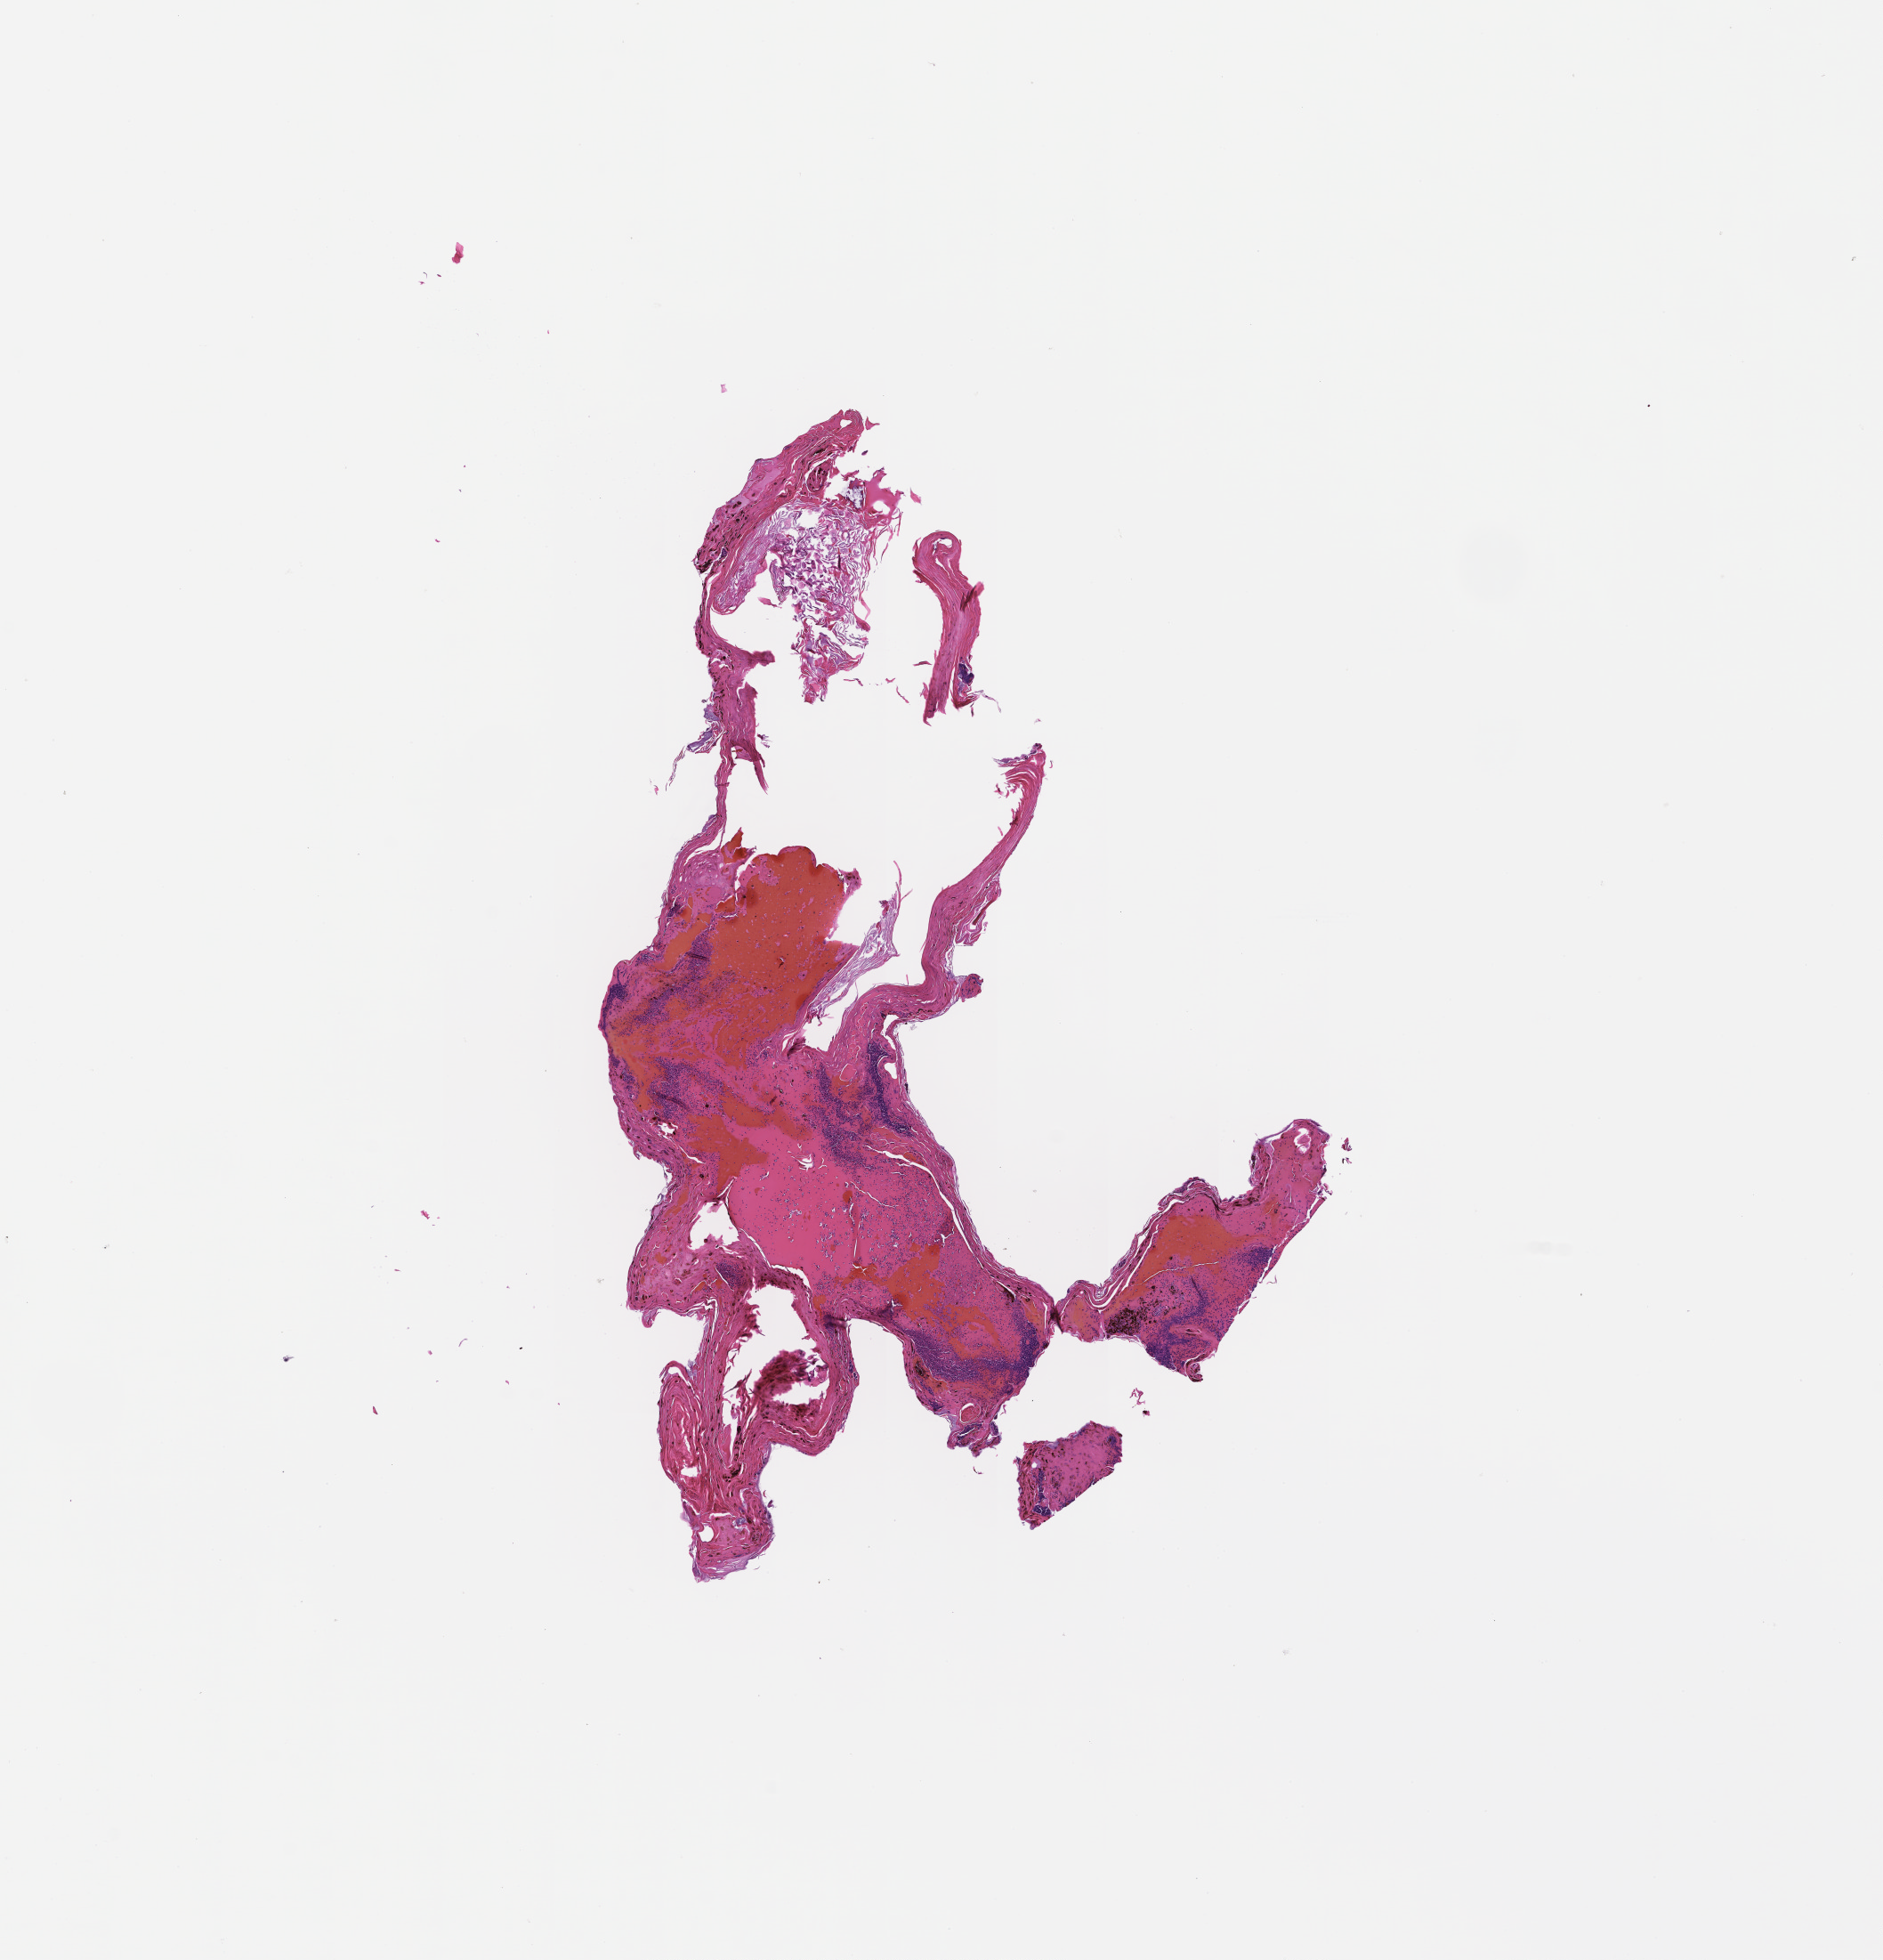
Whole-slide image, H&E stain, a low-resolution overview of the entire scanned area, about 8.5 x 8.9 mm. FFPE section. Tissue site: skin. Collected at baseline (before treatment). Patient: male.
• this section: primary tumor
• diagnosis: Melanoma